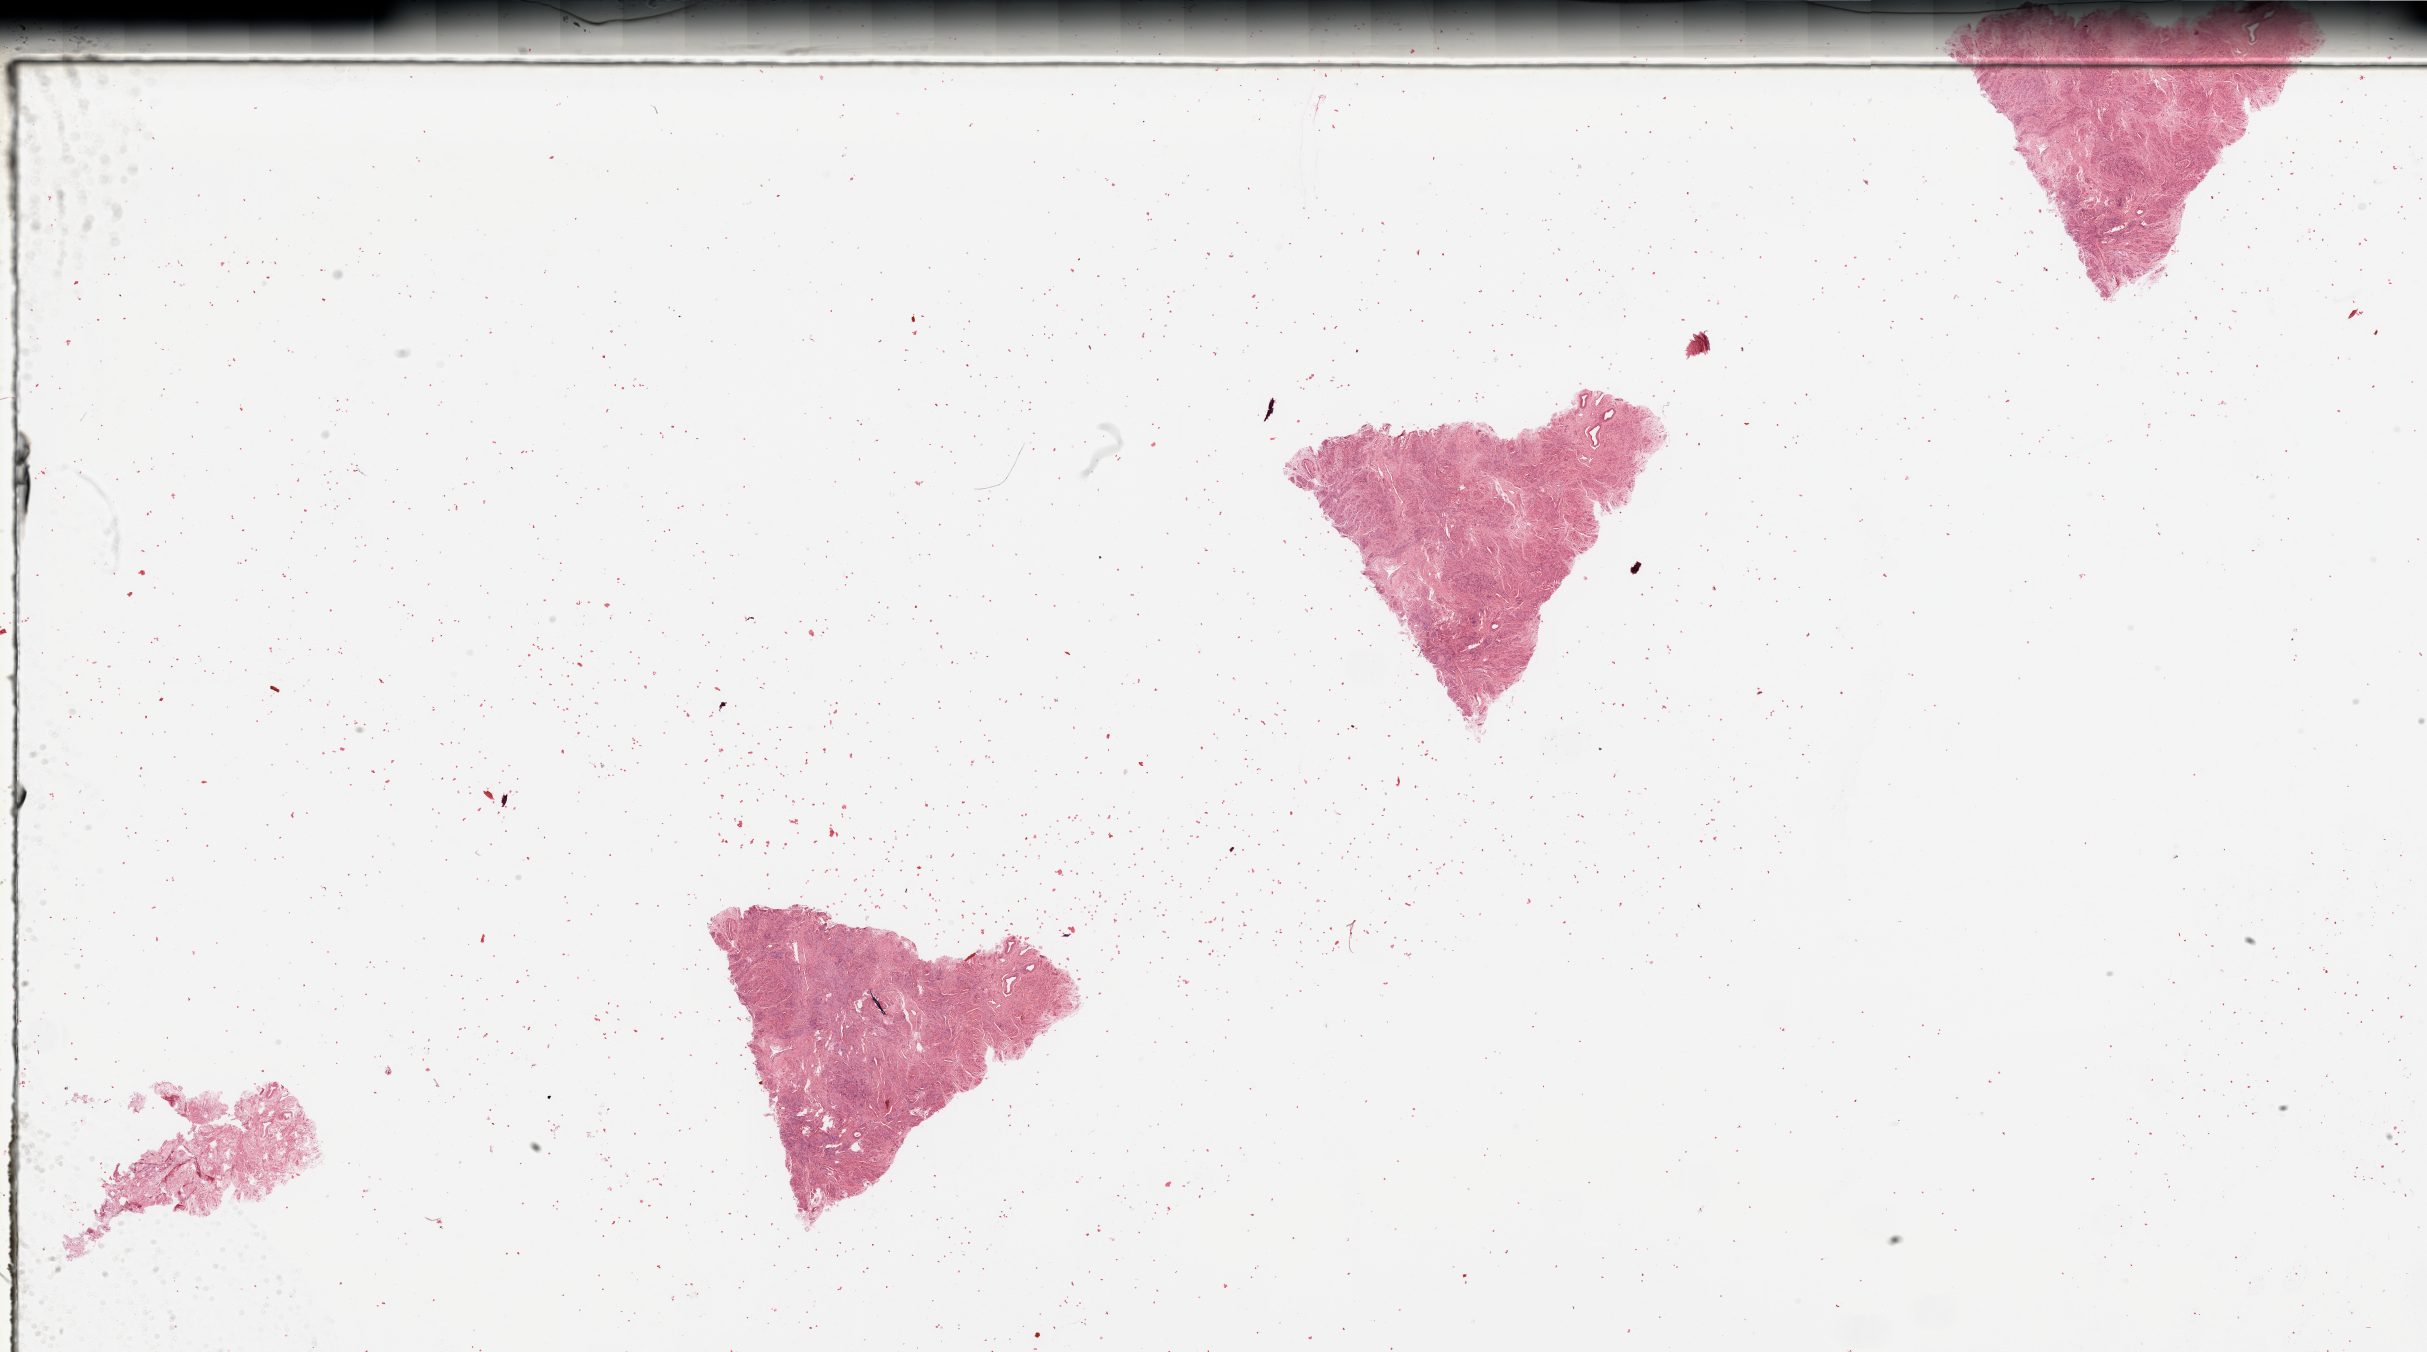
Whole-slide histology image, Hematoxylin and eosin (H&E) stained — whole scanned area (about 38.4 x 21.4 mm) shown as a low-resolution overview; normal (non-tumour) tissue sample, sampled site: uterus. Female, 84 y/o.
This section: normal (non-tumour) tissue from the same patient. Patient diagnosis: Endometrioid adenocarcinoma, NOS.